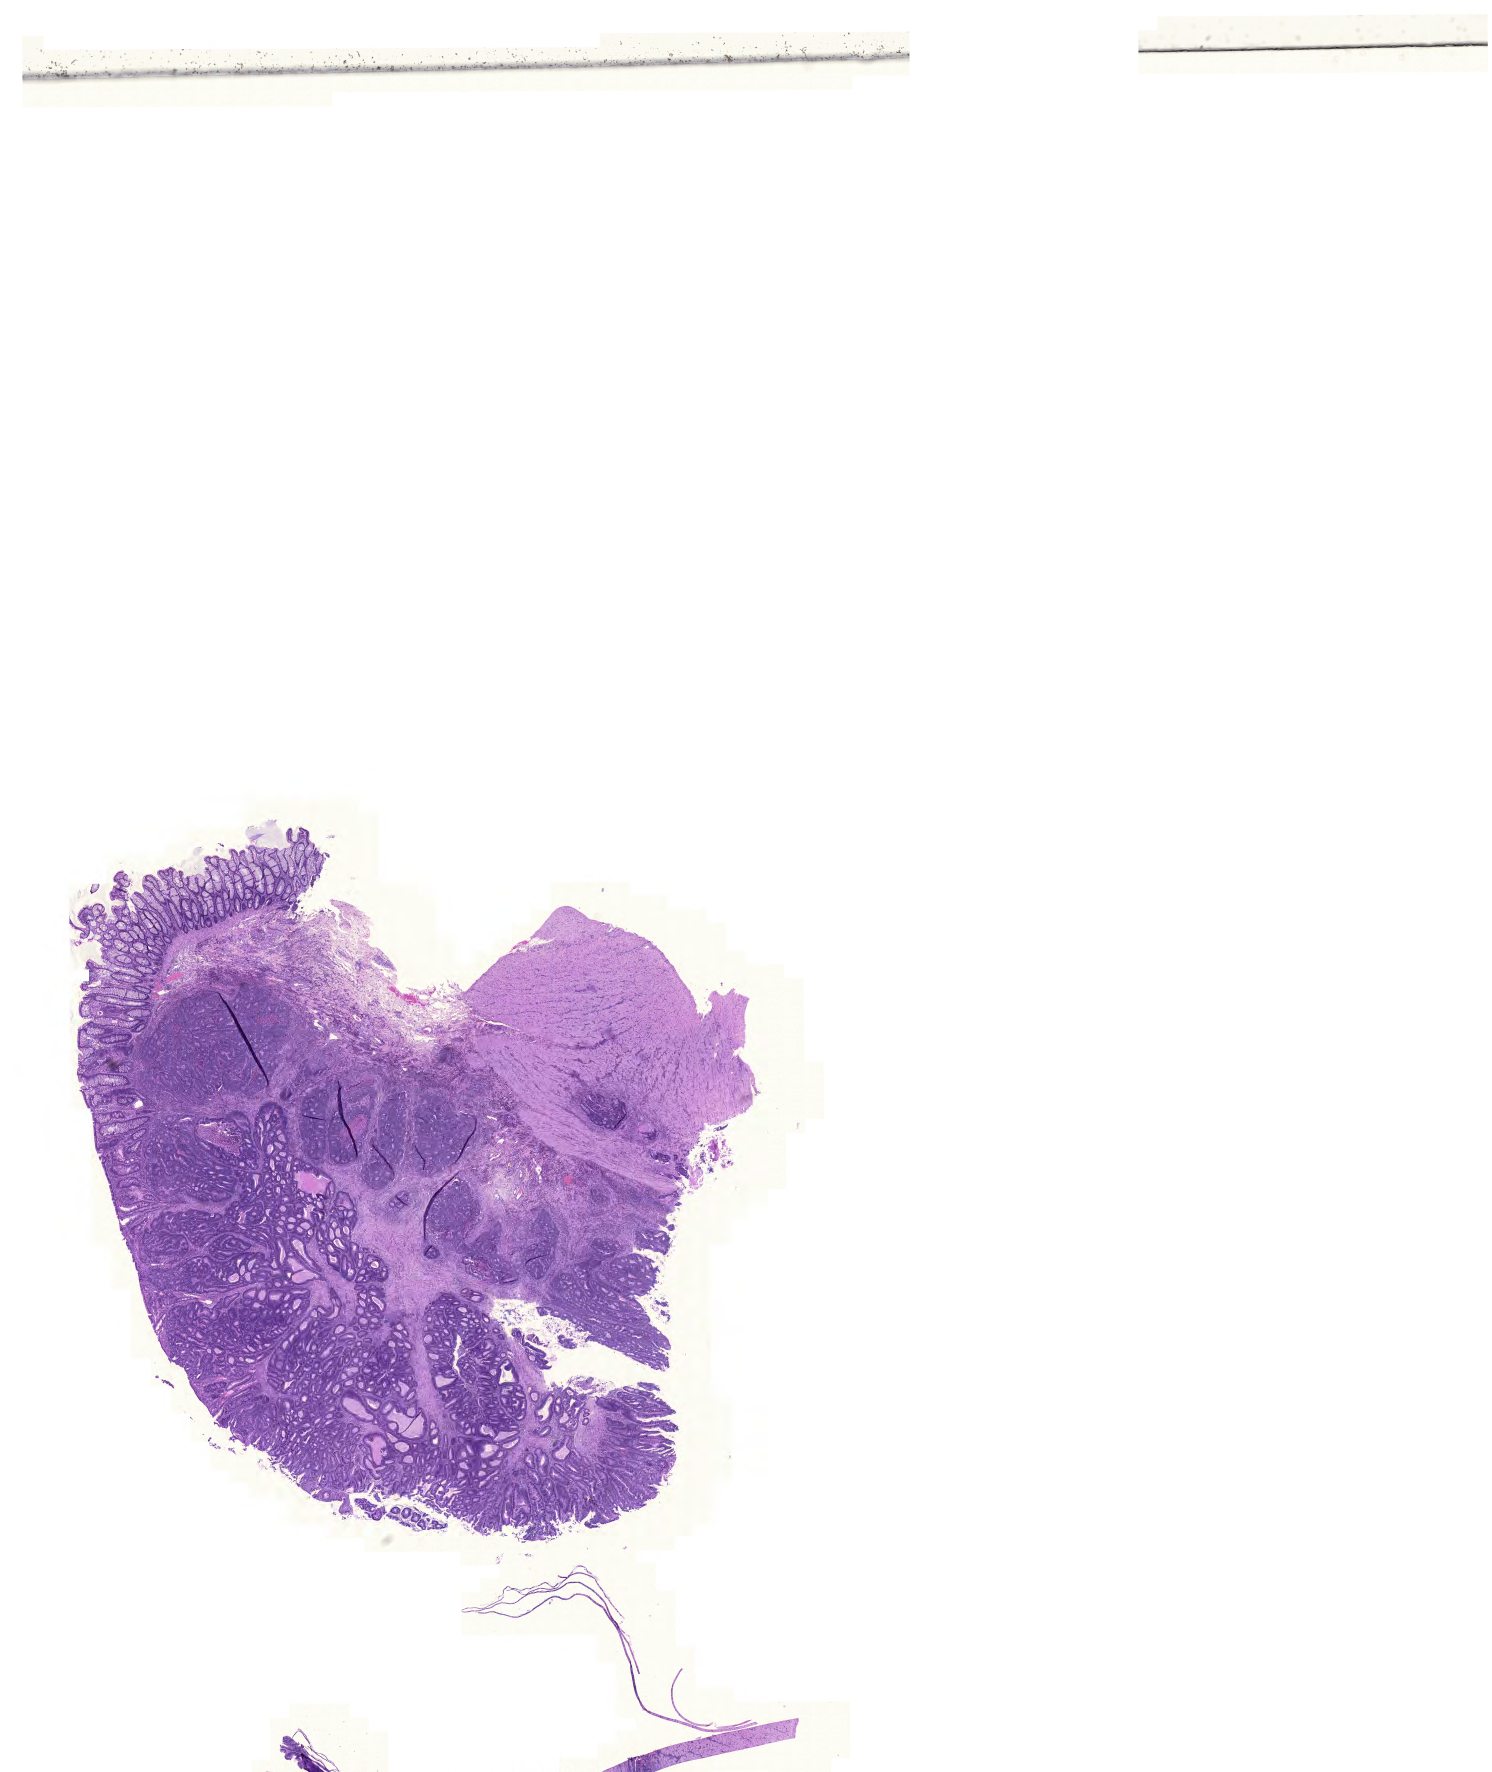
Whole-slide histology image, H&E — whole scanned area (about 22.2 x 26.4 mm) shown as a low-resolution overview. FFPE section. Colon, primary tumour sample. Male, age 58 years at initial diagnosis.
* diagnosis: Adenocarcinoma, NOS
* lymph nodes positive (case pathology): 2 of 19 examined
* AJCC pathologic stage: III (5th edition)